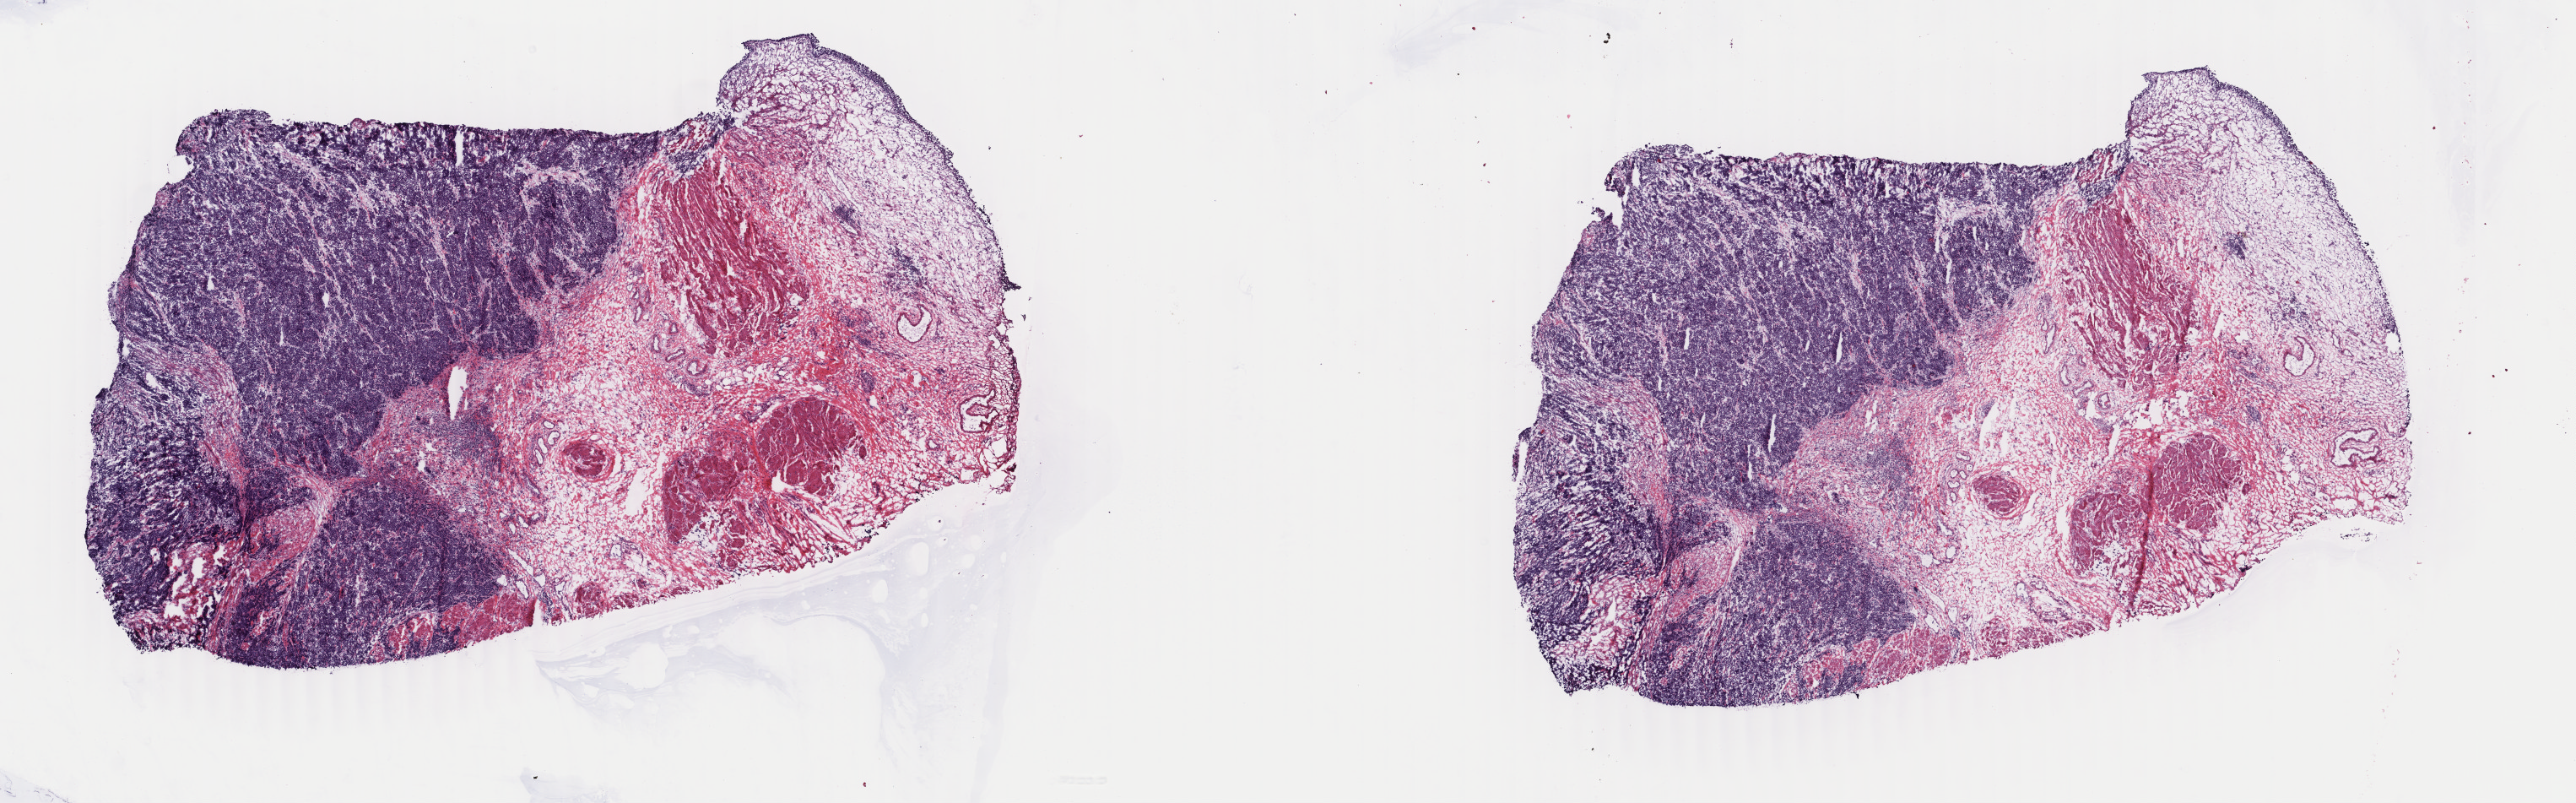
H&E whole-slide image, low-resolution overview of the scanned area, about 24.3 x 7.6 mm (slide scanned at 40x). Frozen section. Bladder, primary tumour sample. Female, age 68 years at initial diagnosis. Histologic grade: high grade. Pathologist review of this section (percent, as recorded): tumour cells 55%, tumour nuclei 80%, normal cells 44%, stromal cells 5%, necrosis 2%. Infiltration values recorded for this section: lymphocyte infiltration 8%, monocyte infiltration 0%, neutrophil infiltration 0%.
- AJCC pathologic stage: IV
- diagnosis: Transitional cell carcinoma